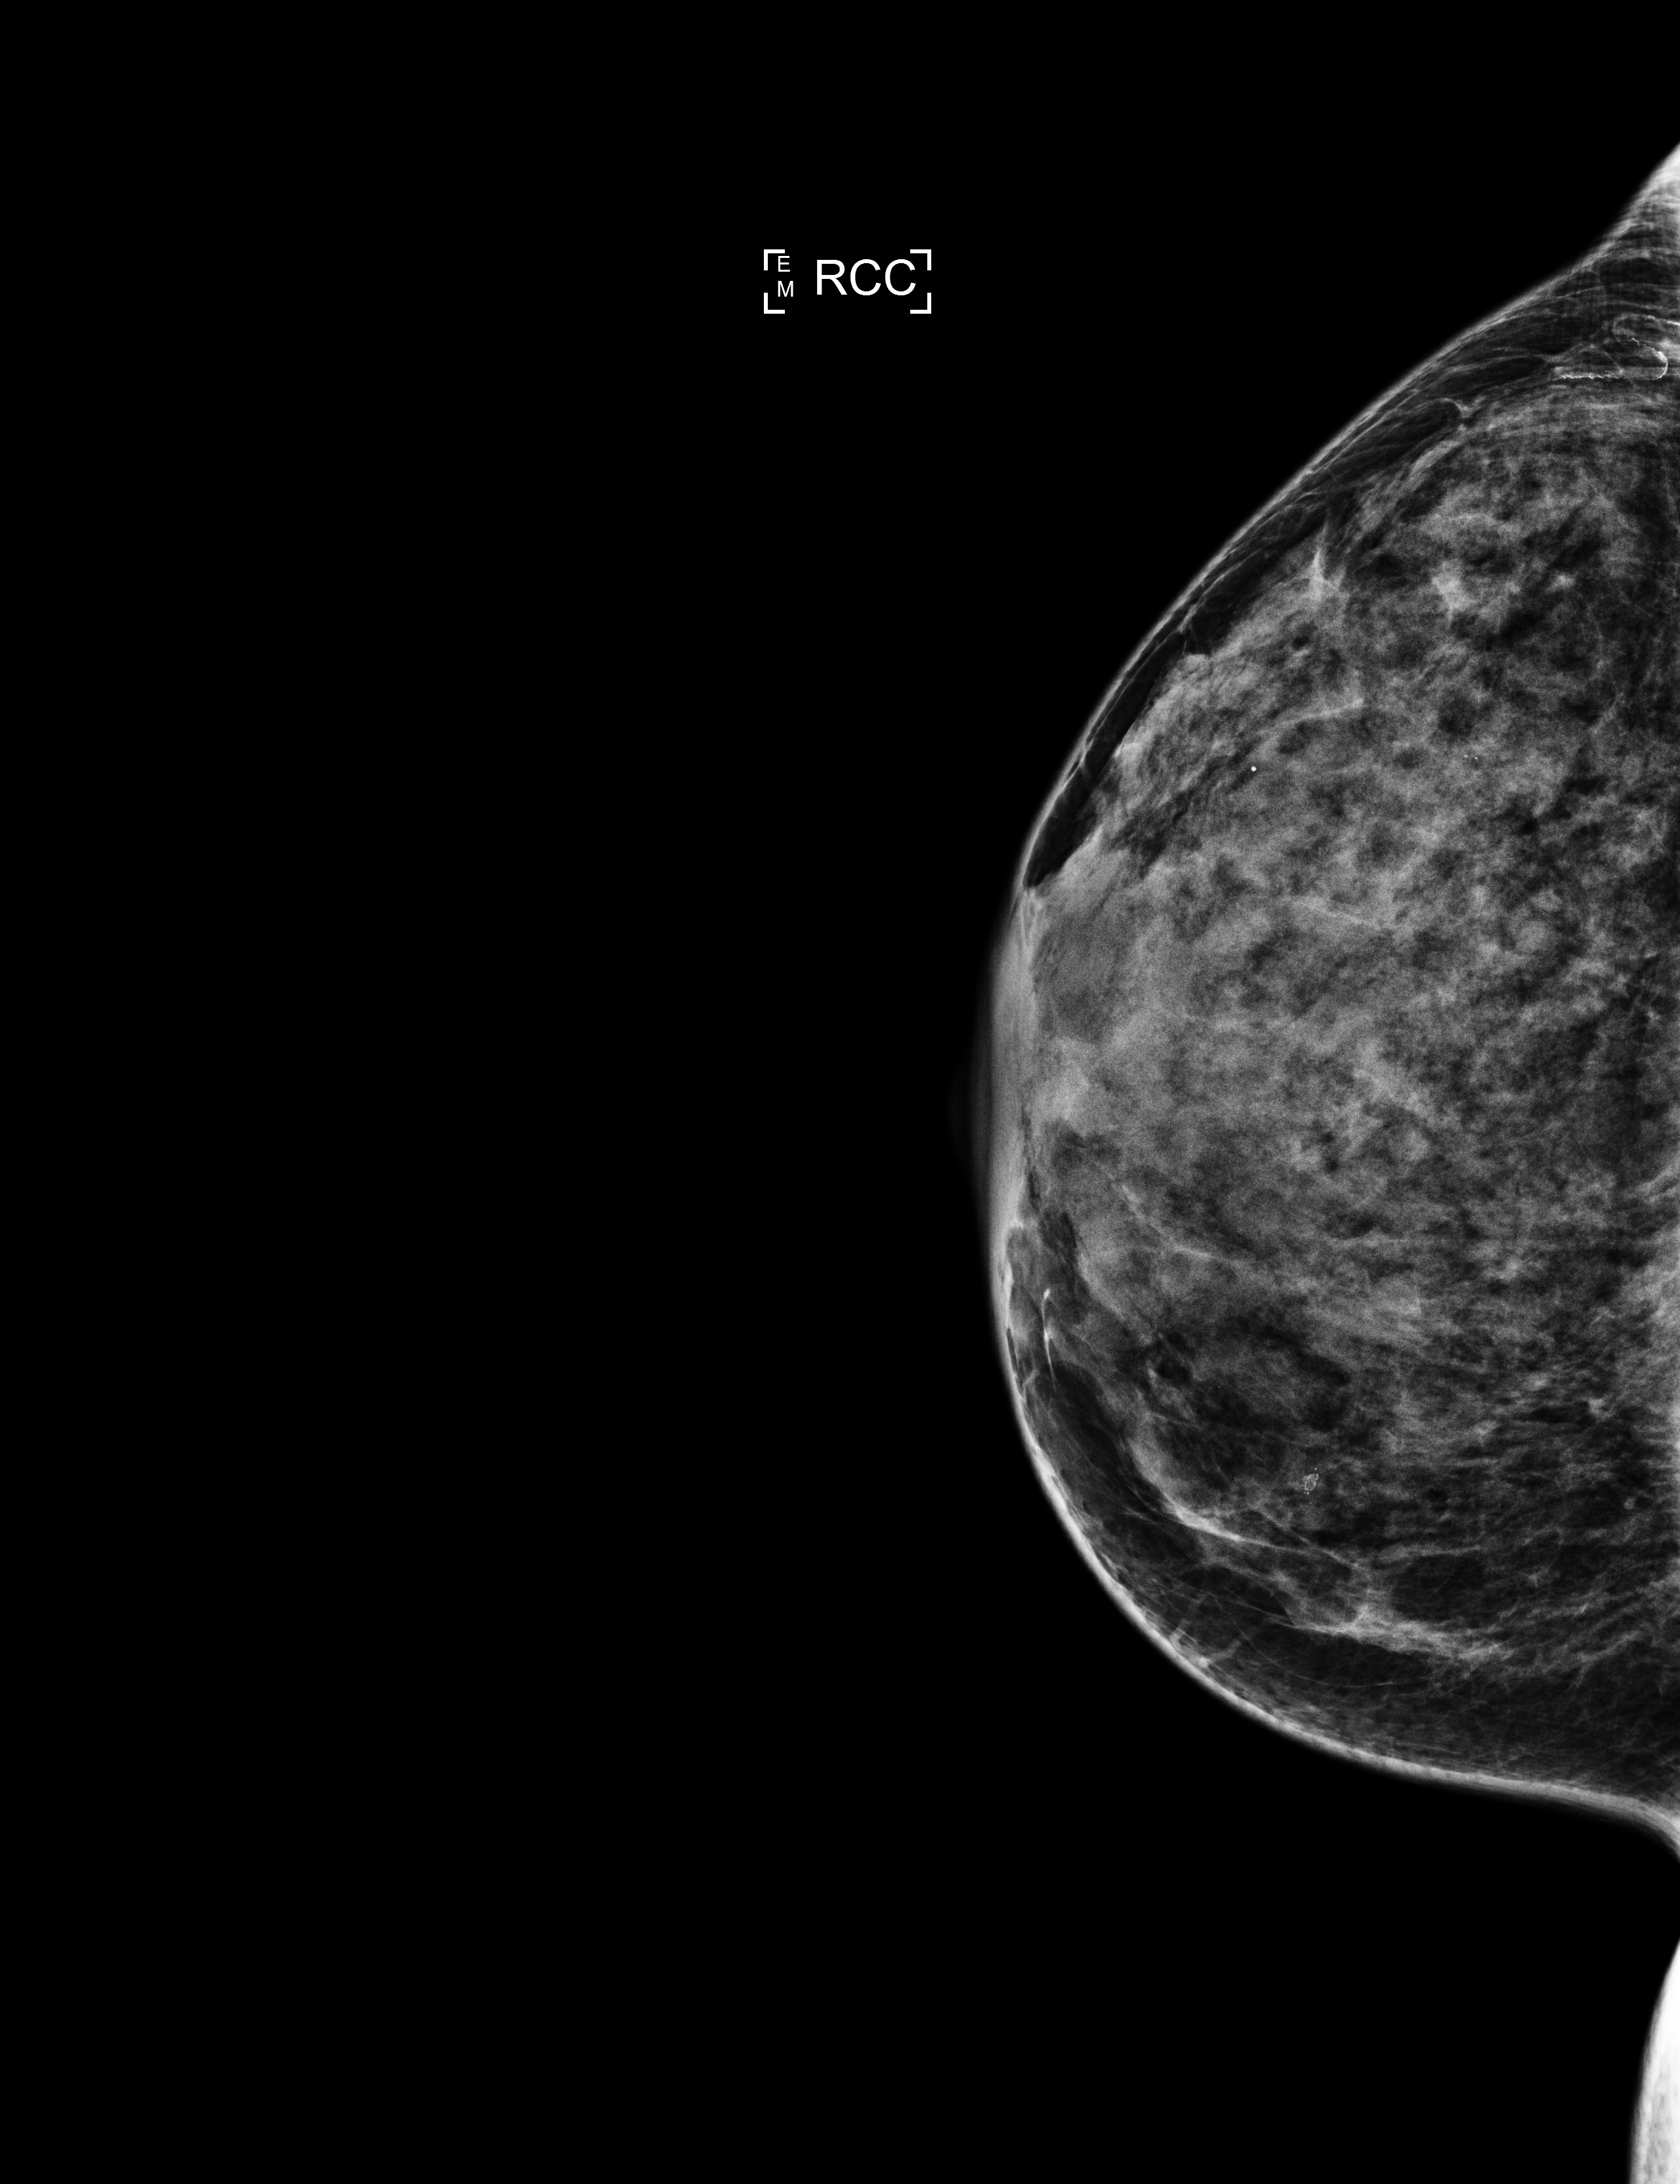
Screening examination, system: Selenia Dimensions. Patient aged 57 years (female).
Image type: full-field digital mammogram. Breast: right. Projection: craniocaudal (CC) view.